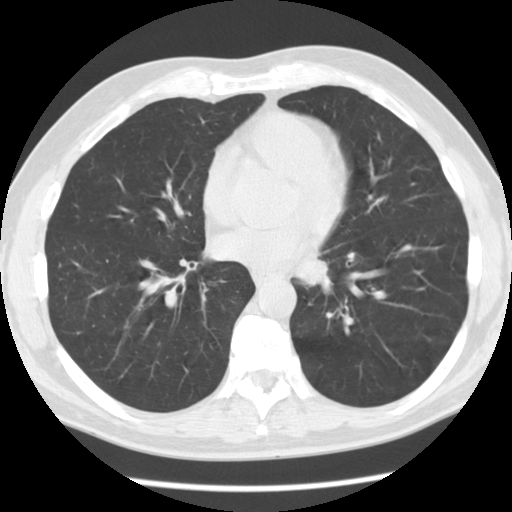
Low-dose screening chest CT, axial slice; baseline screening round; lung window (W 1500 / L -600 HU); 2.5 mm slice thickness; standard (soft-tissue) reconstruction kernel (STANDARD). Male, age 55 years at enrolment. Former smoker at enrolment.
Lesion marked by an expert reader, bounding box (x1, y1, x2, y2) in pixels: (284, 235, 346, 296). Screening reader's record for this exam: no non-calcified nodule ≥4 mm recorded. Official screen result: negative screen, minor abnormalities not suspicious for lung cancer. Later outcome: lung cancer diagnosed 223 days after this screen — squamous cell carcinoma, NOS, left lower lobe, moderately differentiated (G2), stage IV (AJCC 6th edition), 51 mm at pathology.